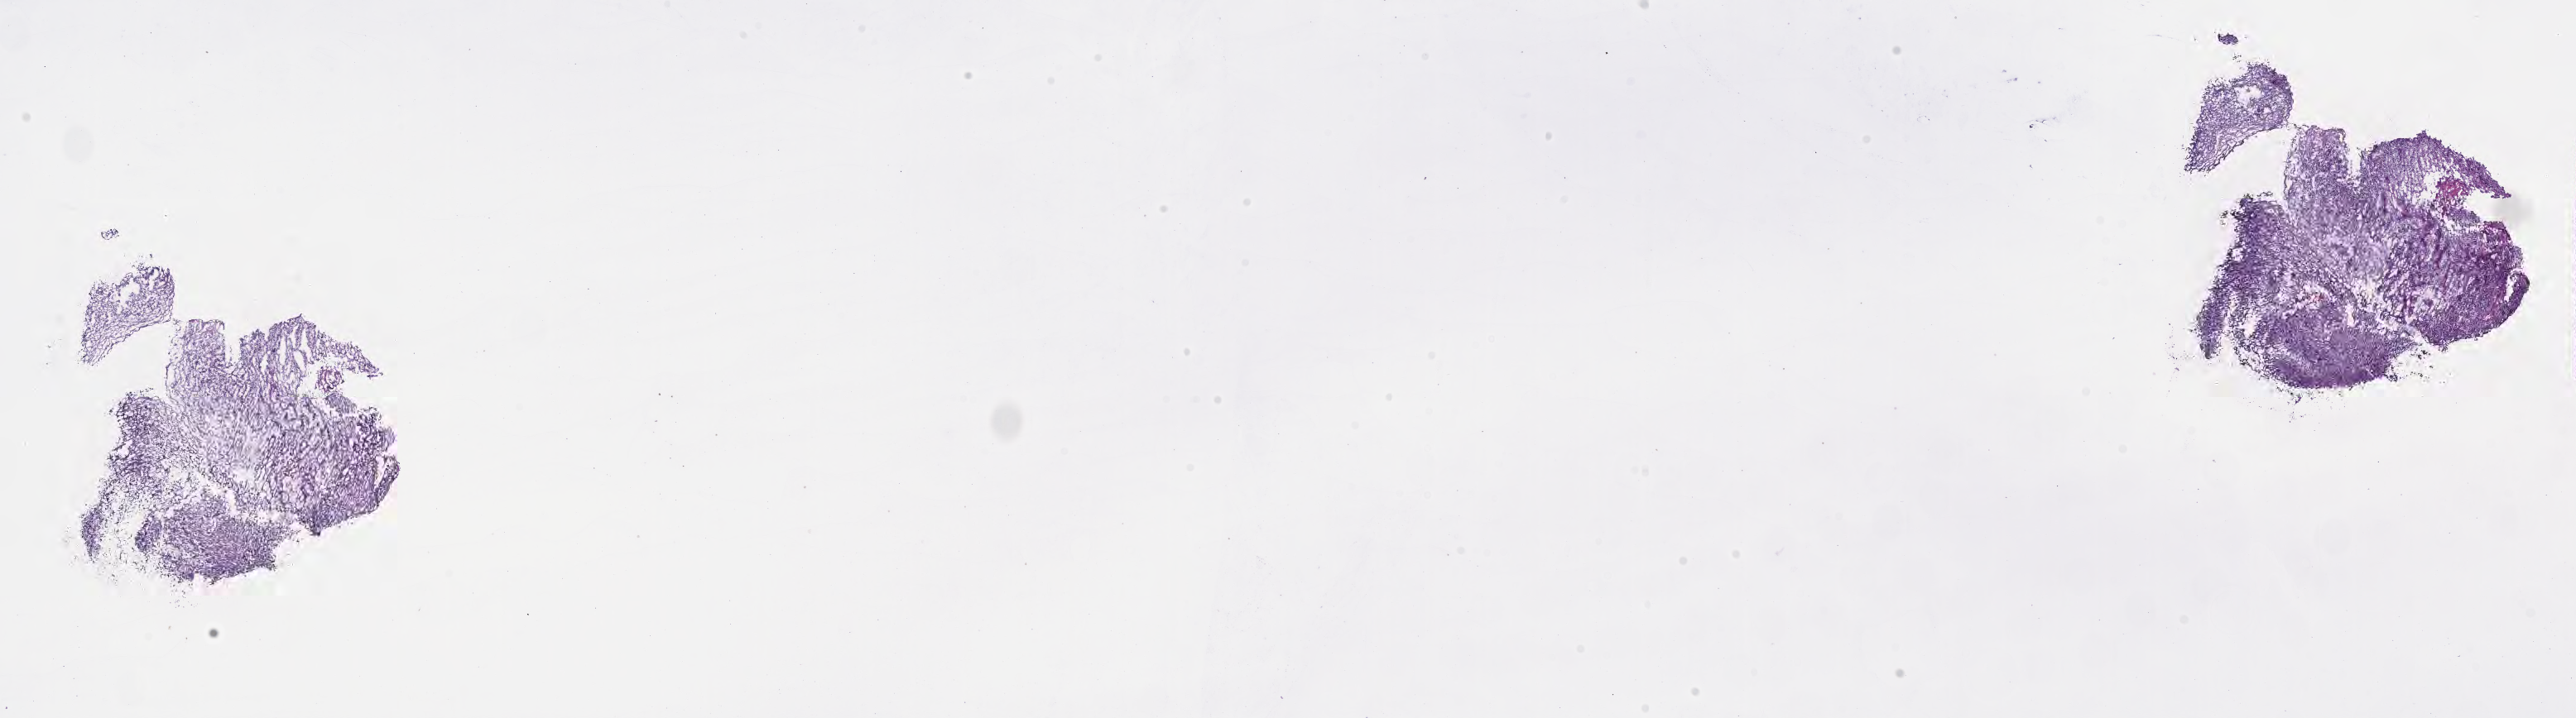
Digitized haematoxylin and eosin-stained section of tumor tissue from the orbit, a low-resolution overview of the entire scanned area, about 25.2 x 7.0 mm, cryosection (OCT / tissue freezing medium). Female patient, age 972 days (about 2.7 years).
Diagnosis (ICD-O-3 morphology term): Rhabdomyosarcoma, NOS.